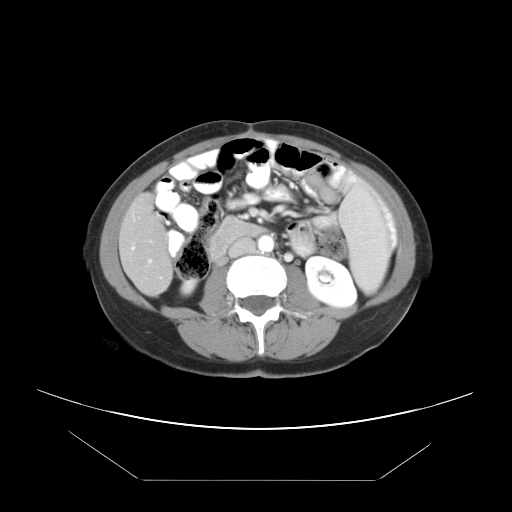
Contrast-enhanced abdominal CT, one axial slice; position 11 of 45 along the scan axis; intravenous contrast given; soft-tissue window (W 400 / L 40 HU); 5 mm slice thickness; 512 × 512 image matrix, field of view 405 × 405 mm. Female patient, age 52 years. Case-level facts recorded for this patient, not image findings: diagnosis: colorectal cancer liver metastases, imaged before liver resection; multiple liver metastases: yes; largest metastasis: 2.5 cm; chemotherapy before resection: yes.
Annotated regions visible in this slice (outlined manually by an expert reader):
- hepatic veins: bounding box <132,247,135,250> (left, top, right, bottom; pixels)
- liver: <120,197,171,295>
- planned liver remnant (the part of the liver to remain after resection): <120,197,164,253>
- portal vein (with intrahepatic branches): <148,258,153,265>